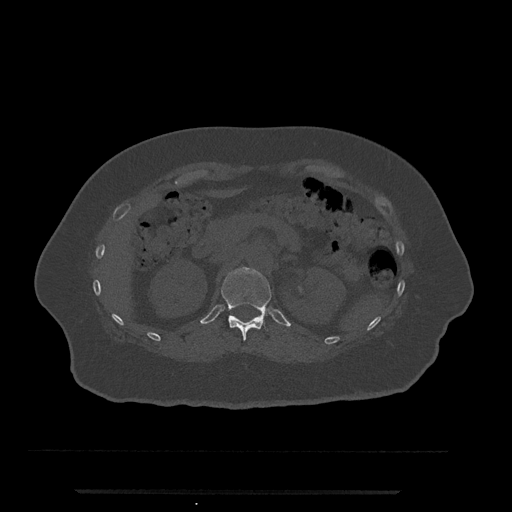
CT including the spine, one axial slice. Slice 163 of 797 in the series (ordered by position). Reconstruction kernel Br40s/3. Bone window (W 1800 / L 400 HU). 0.5 mm slice thickness. 512 × 512 image matrix, field of view 440 × 440 mm. Female patient, age 51 years. From the clinical record (not read from this slice): primary cancer: neuro.
Annotated regions visible in this slice (semi-automatic segmentation, software-assisted and operator-edited):
- T12 vertebra: bounding box [x1, y1, x2, y2] px = [221, 267, 271, 341]